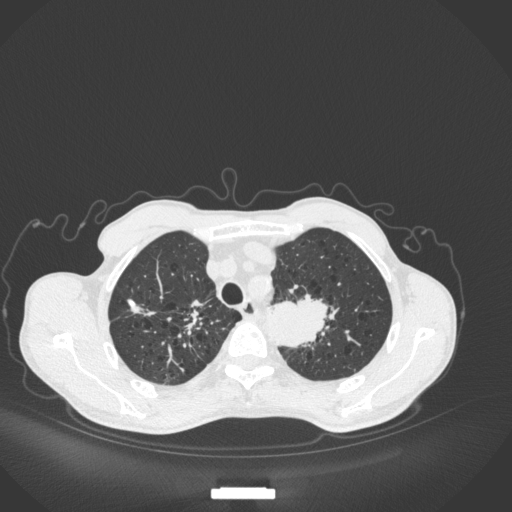
Chest CT, one axial slice. Slice 346 of 394 in the series (ordered by position). 120 kVp. Lung window (W 1500 / L -600 HU). 512 × 512 image matrix. Male patient, age 65 years. From the clinical record (not read from this slice): clinical TNM (as recorded): T2b N0 M0; histopathological grade: G2.
Outlined on this slice (bounding box drawn by a radiologist):
- lung tumour (recorded histology: adenocarcinoma): box from (x=269, y=288) to (x=329, y=353) px